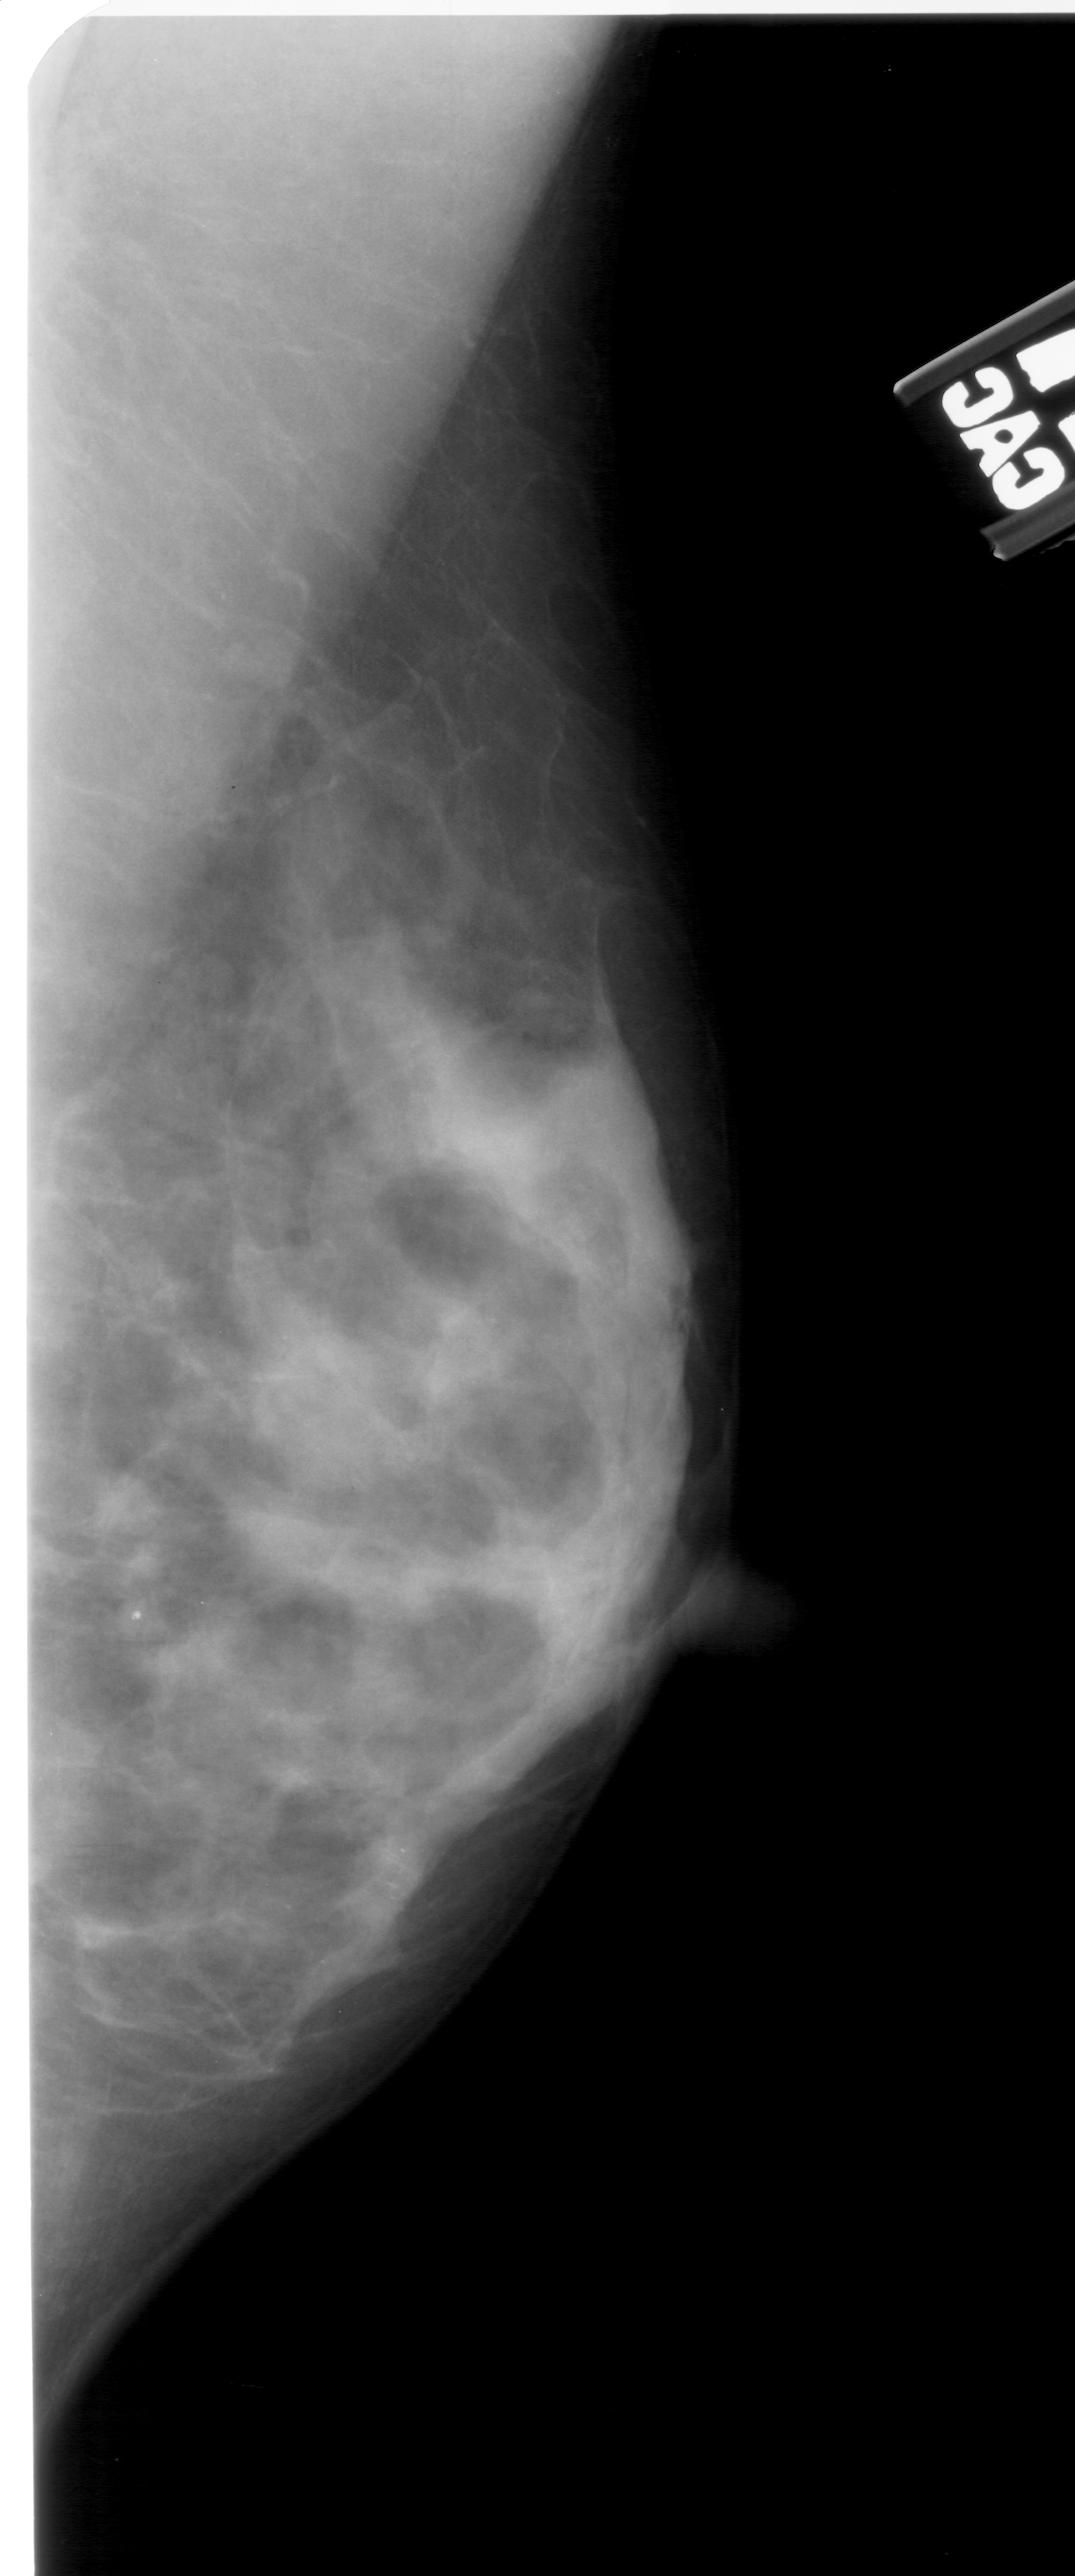
Mammogram (digitized film); right breast; mediolateral oblique (MLO) view; BI-RADS breast density category 4 (scale 1–4); 1075 × 2576 image matrix.
Expert-marked regions of interest on this image (one box per marked abnormality):
- calcifications, morphology pleomorphic, distribution clustered; BI-RADS assessment category 4; pathology (as recorded): benign: bounding box [x1, y1, x2, y2] px = [368, 1833, 433, 1926]